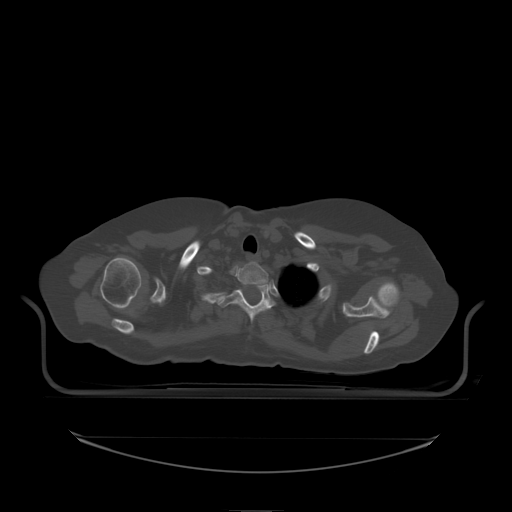
CT including the spine, one axial slice; slice 182 of 242 in the series (ordered by position); bone window (W 1800 / L 400 HU); 2.5 mm slice thickness; 512 × 512 image matrix, field of view 500 × 500 mm. Patient: female, 53 years. From the clinical record (not read from this slice): primary cancer: lung; vertebrae with lytic lesions (as recorded): T7, L1.
Structures marked on this image (semi-automatic segmentation, software-assisted and operator-edited):
- T1 vertebra: bounding box [x1, y1, x2, y2] px = [237, 262, 272, 286]
- T2 vertebra: [219, 285, 276, 322]